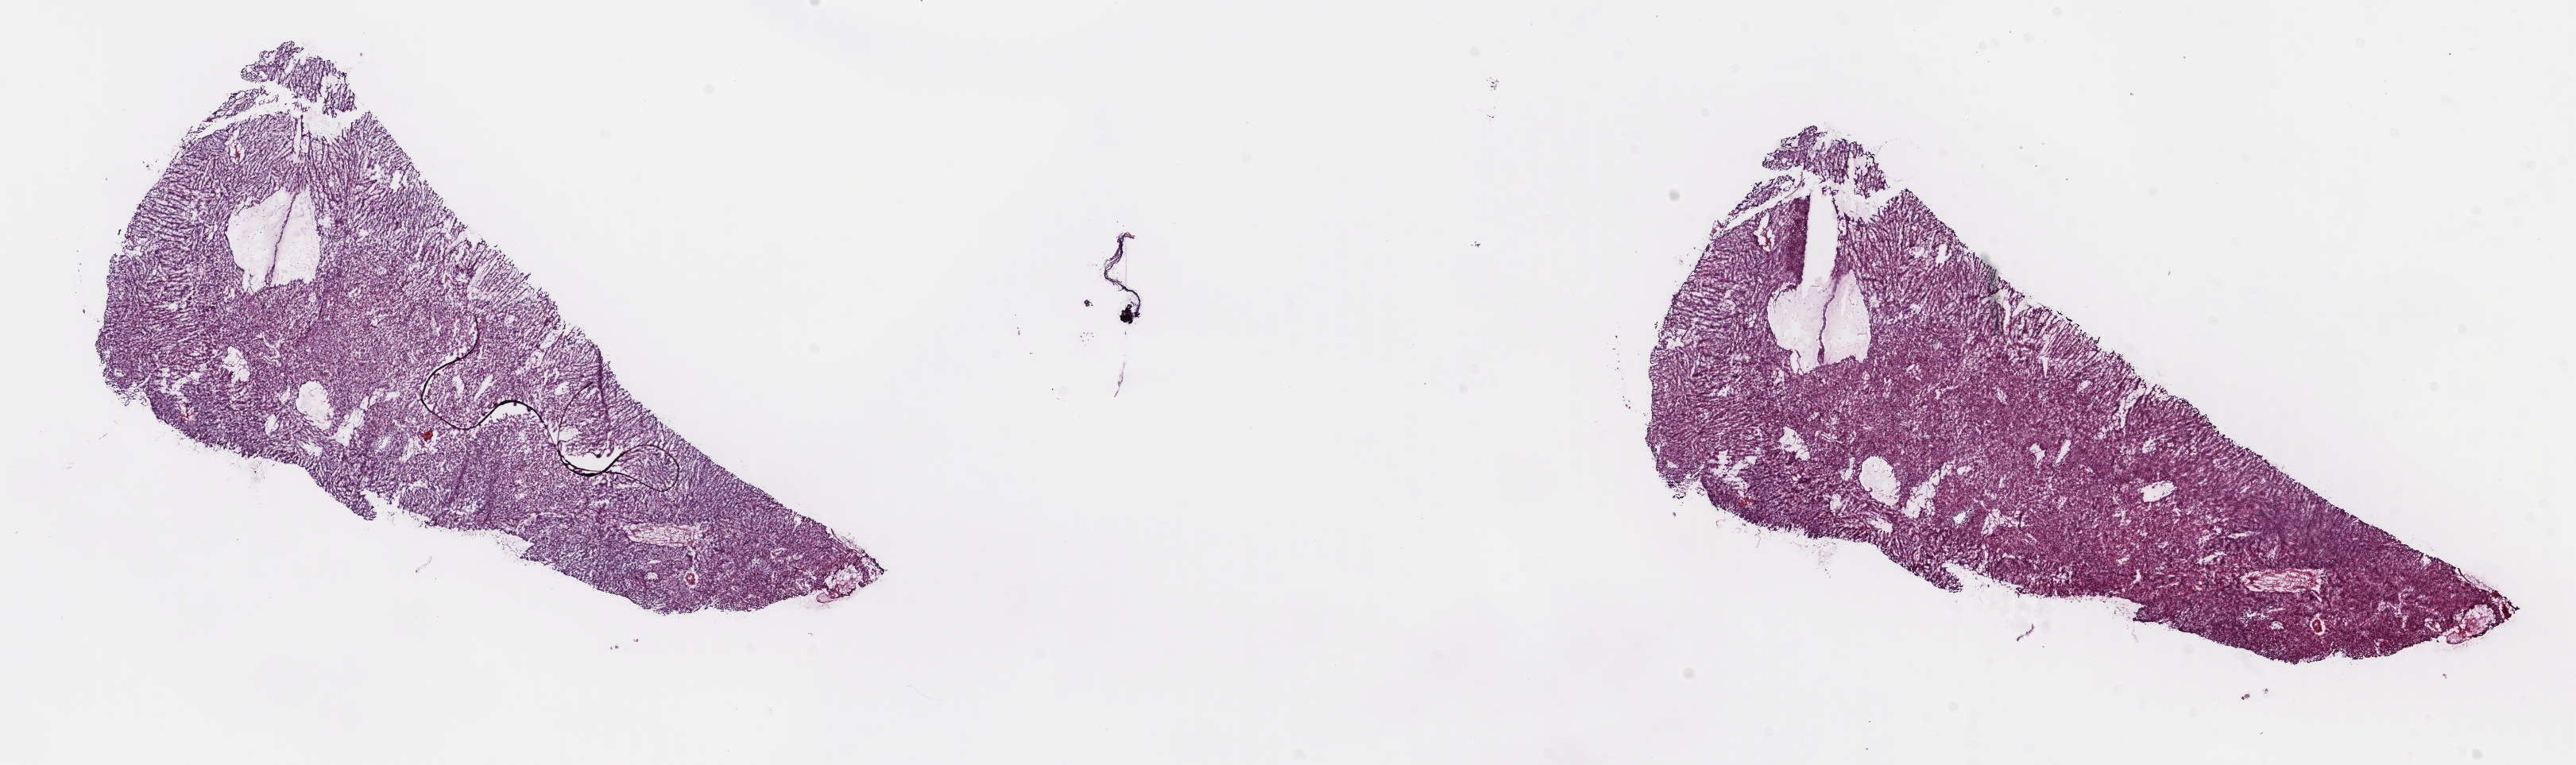
Digitized H&E tissue section (whole slide), a low-resolution overview of the entire scanned area, about 25.5 x 7.6 mm (slide scanned at 40x), frozen section from the top of the tissue portion, sample: primary tumour, uterus. Female patient; age at initial diagnosis 62 years. Slide review estimates, as recorded: tumour cells 90%, tumour nuclei 100%, normal cells 0%, stromal cells 10%, necrosis 0%. Inflammatory infiltration, as recorded: lymphocyte infiltration 0%, monocyte infiltration 0%, neutrophil infiltration 0%.
- pathologic diagnosis: Leiomyosarcoma, NOS